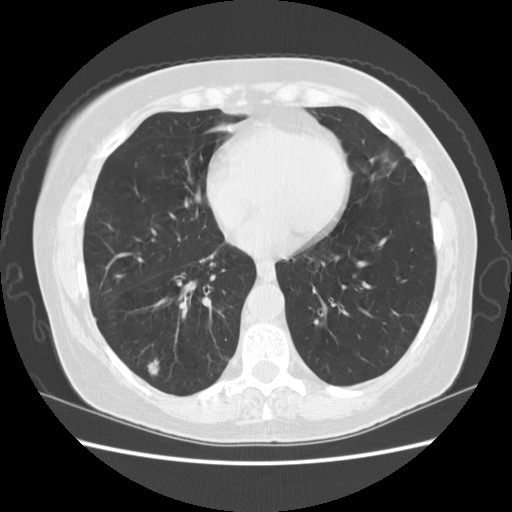
Chest CT (low-dose screening protocol), one axial image. Third screening round (two years after baseline). Lung window (W 1500 / L -600 HU). Standard (soft-tissue) reconstruction kernel (STANDARD). Female, age 59 years at enrolment. Current smoker at enrolment.
- Expert-annotated lung lesion, bounding box [x1, y1, x2, y2] px = [133, 351, 173, 387].
- The exam's reader record, not a measurement of the box and not confirmed to be the same lesion: non-calcified nodule or mass ≥4 mm, right lower lobe, 16 × 11 mm, smooth margins, soft tissue attenuation, pre-existing on the prior screen: yes; interval growth: yes.
- Official screen result: positive, other.
- Later outcome: lung cancer diagnosed 42 days after this screen — non-small cell carcinoma, right lower lobe, poorly differentiated (G3), stage IA (AJCC 6th edition), 15 mm at pathology.